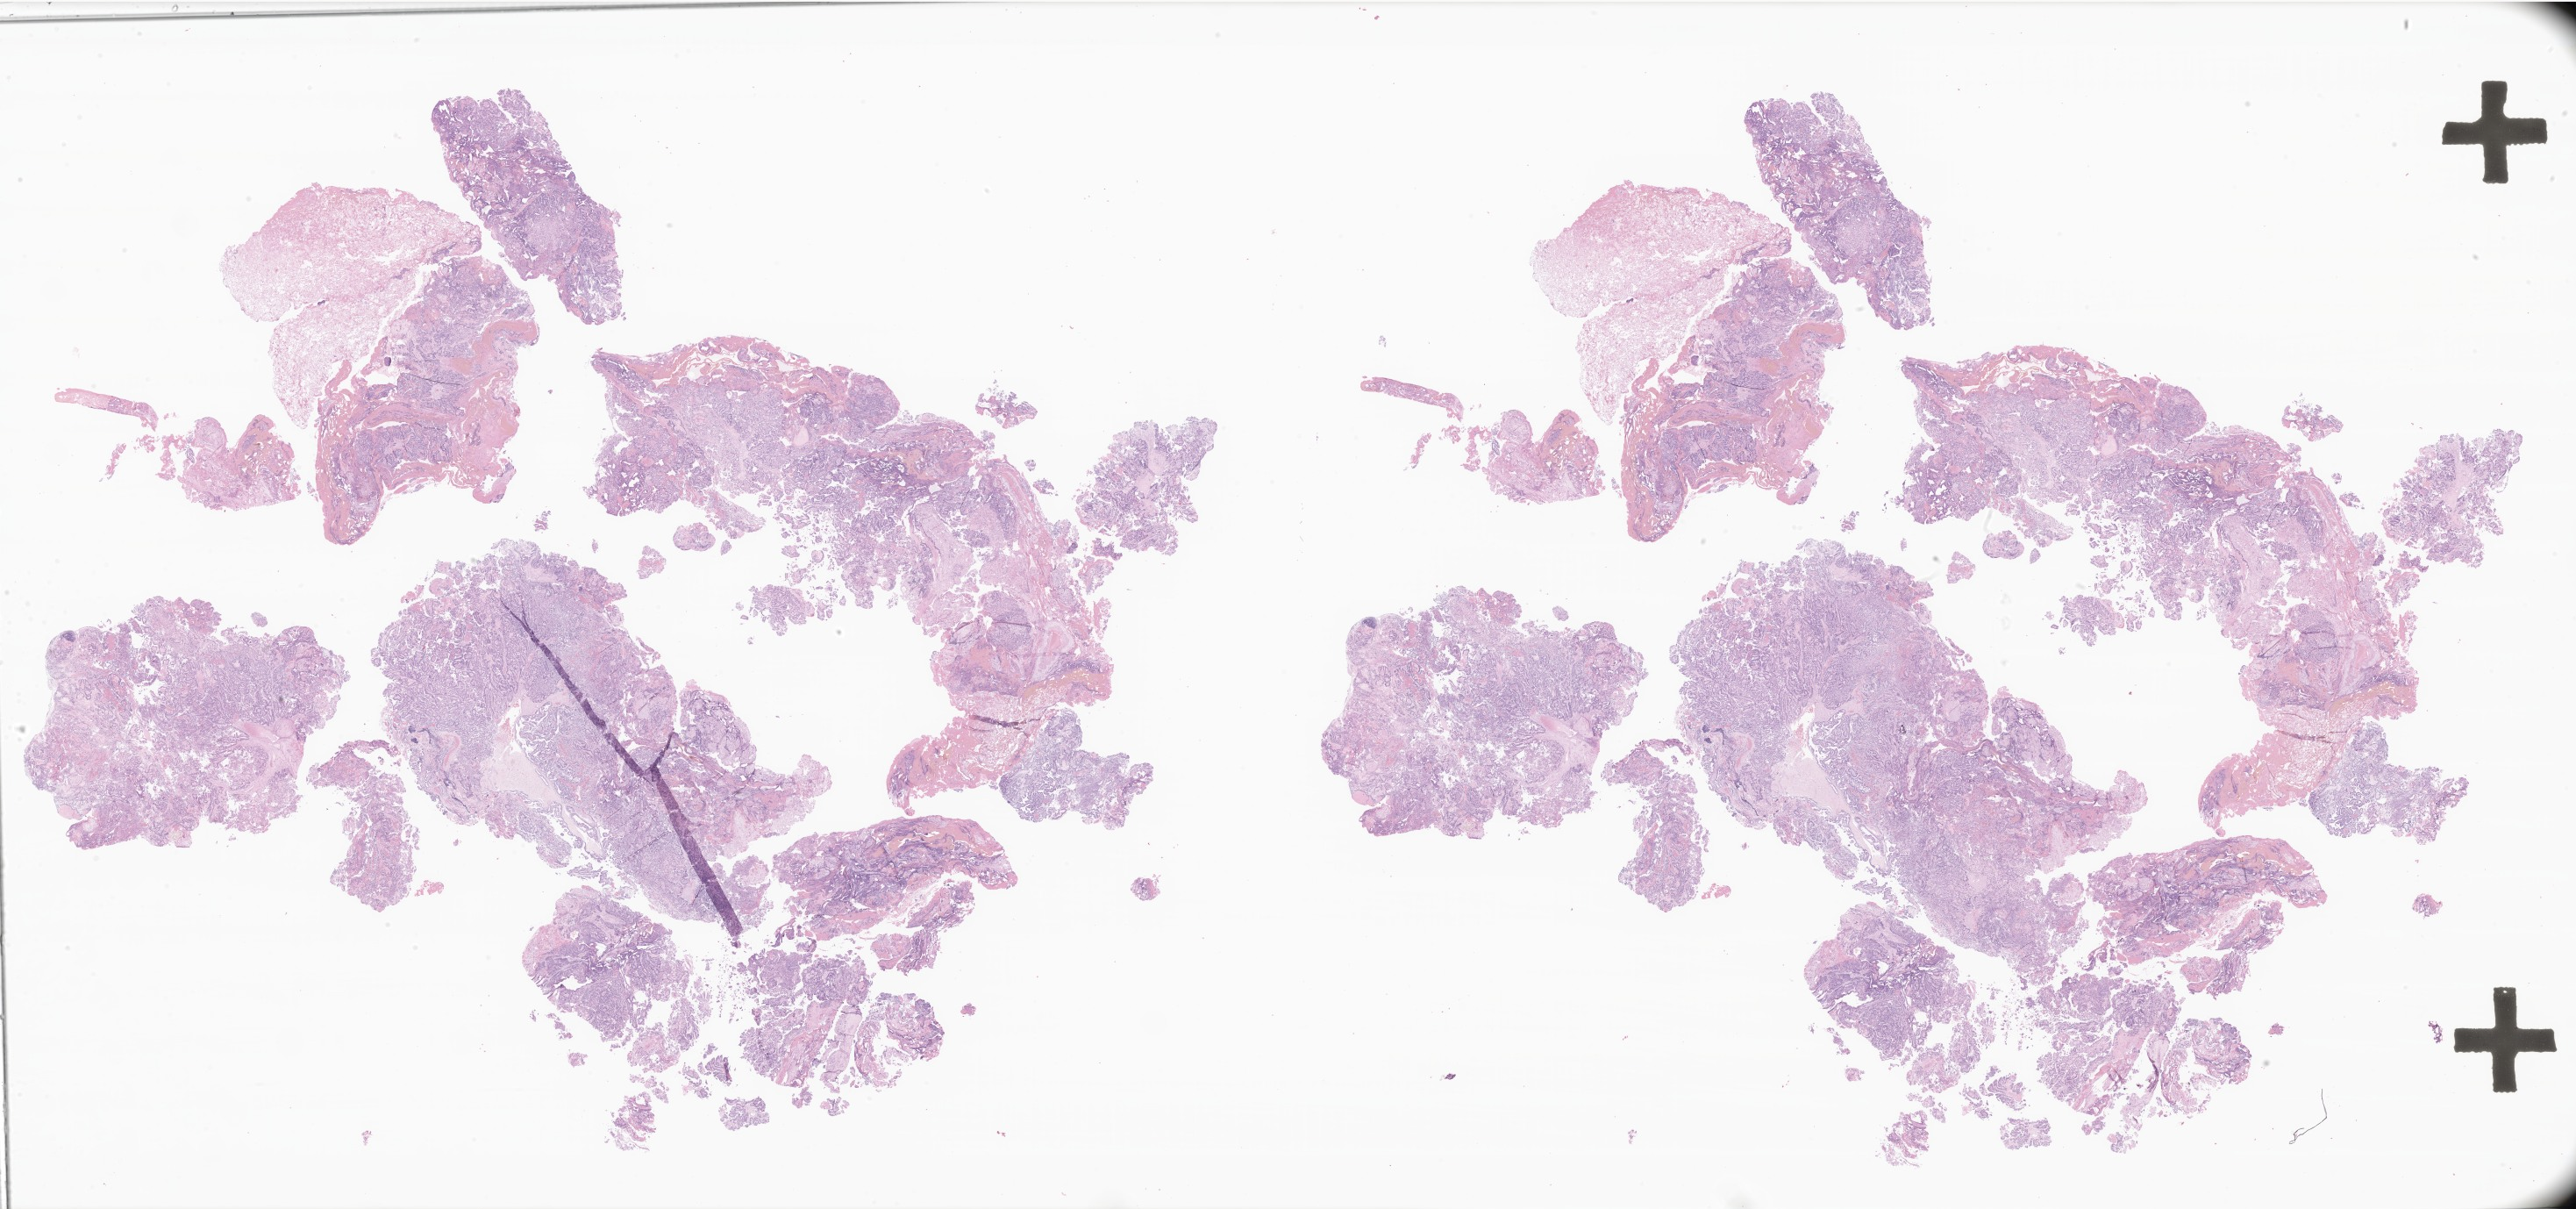
Haematoxylin and eosin whole-slide image of tumor tissue from the cerebral ventricle — a low-resolution overview of the entire scanned area, about 49.5 x 23.2 mm, formalin-fixed, paraffin-embedded (FFPE) tissue. Female patient, age 60 months.
- recorded diagnosis: Choroid plexus papilloma, NOS